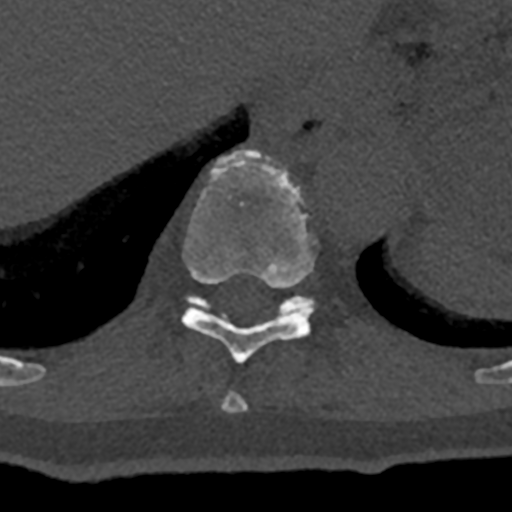
CT including the spine, one axial slice; position 594 of 797 along the scan axis; 120 kVp; bone window (W 1800 / L 400 HU); 512 × 512 image matrix, field of view 160 × 160 mm. Patient: male, 74 years. Case-level facts recorded for this patient, not image findings: primary cancer: renal; vertebrae with lytic lesions (as recorded): T10, L1, L2, L3, L4, L5.
Annotated regions visible in this slice (semi-automatic segmentation, software-assisted and operator-edited):
- T10 vertebra: bounding box <182,150,317,363> (left, top, right, bottom; pixels)
- T11 vertebra: <186,295,315,318>
- T9 vertebra: <222,391,248,413>